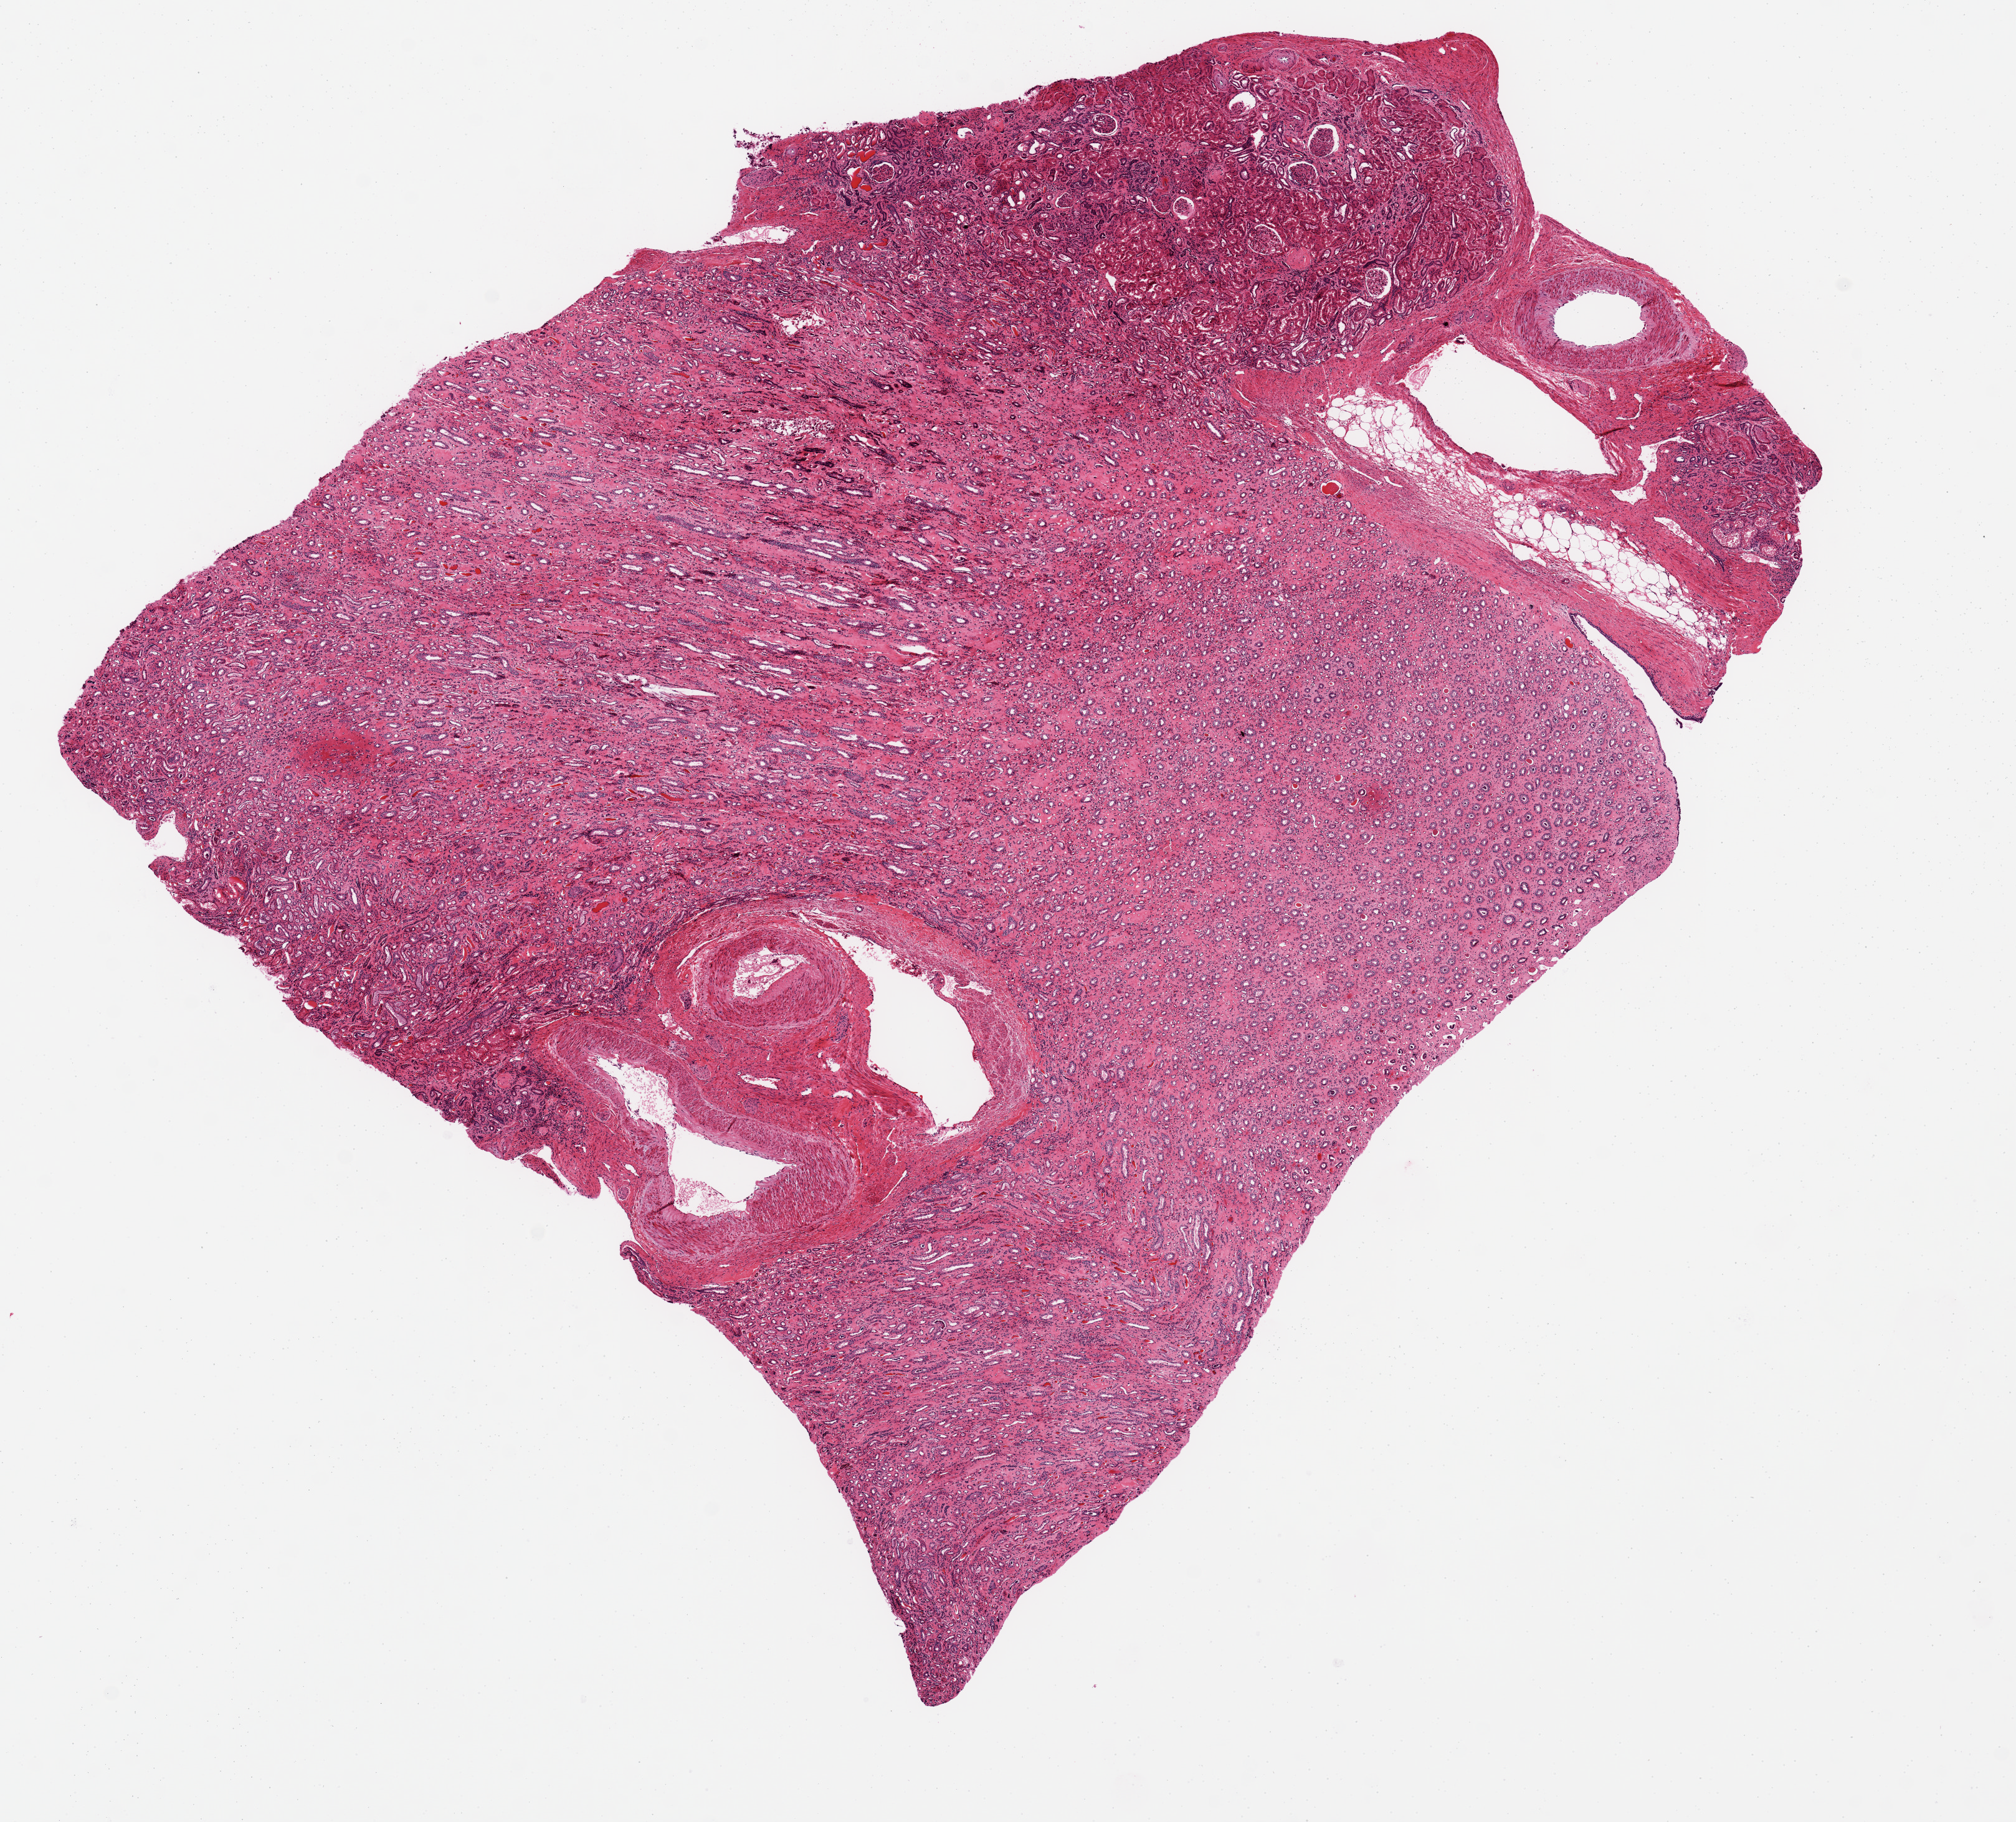
Digitized haematoxylin and eosin-stained section — low-resolution overview of the scanned area, about 12.8 x 11.6 mm. PAXgene-fixed, paraffin-embedded tissue. Sampled site (target tissue): renal medulla. Donor tissue sample. Donor sex: male.
Reviewer comment on this tissue sample: Prominent interstitial fibrosis (See Attachment B).